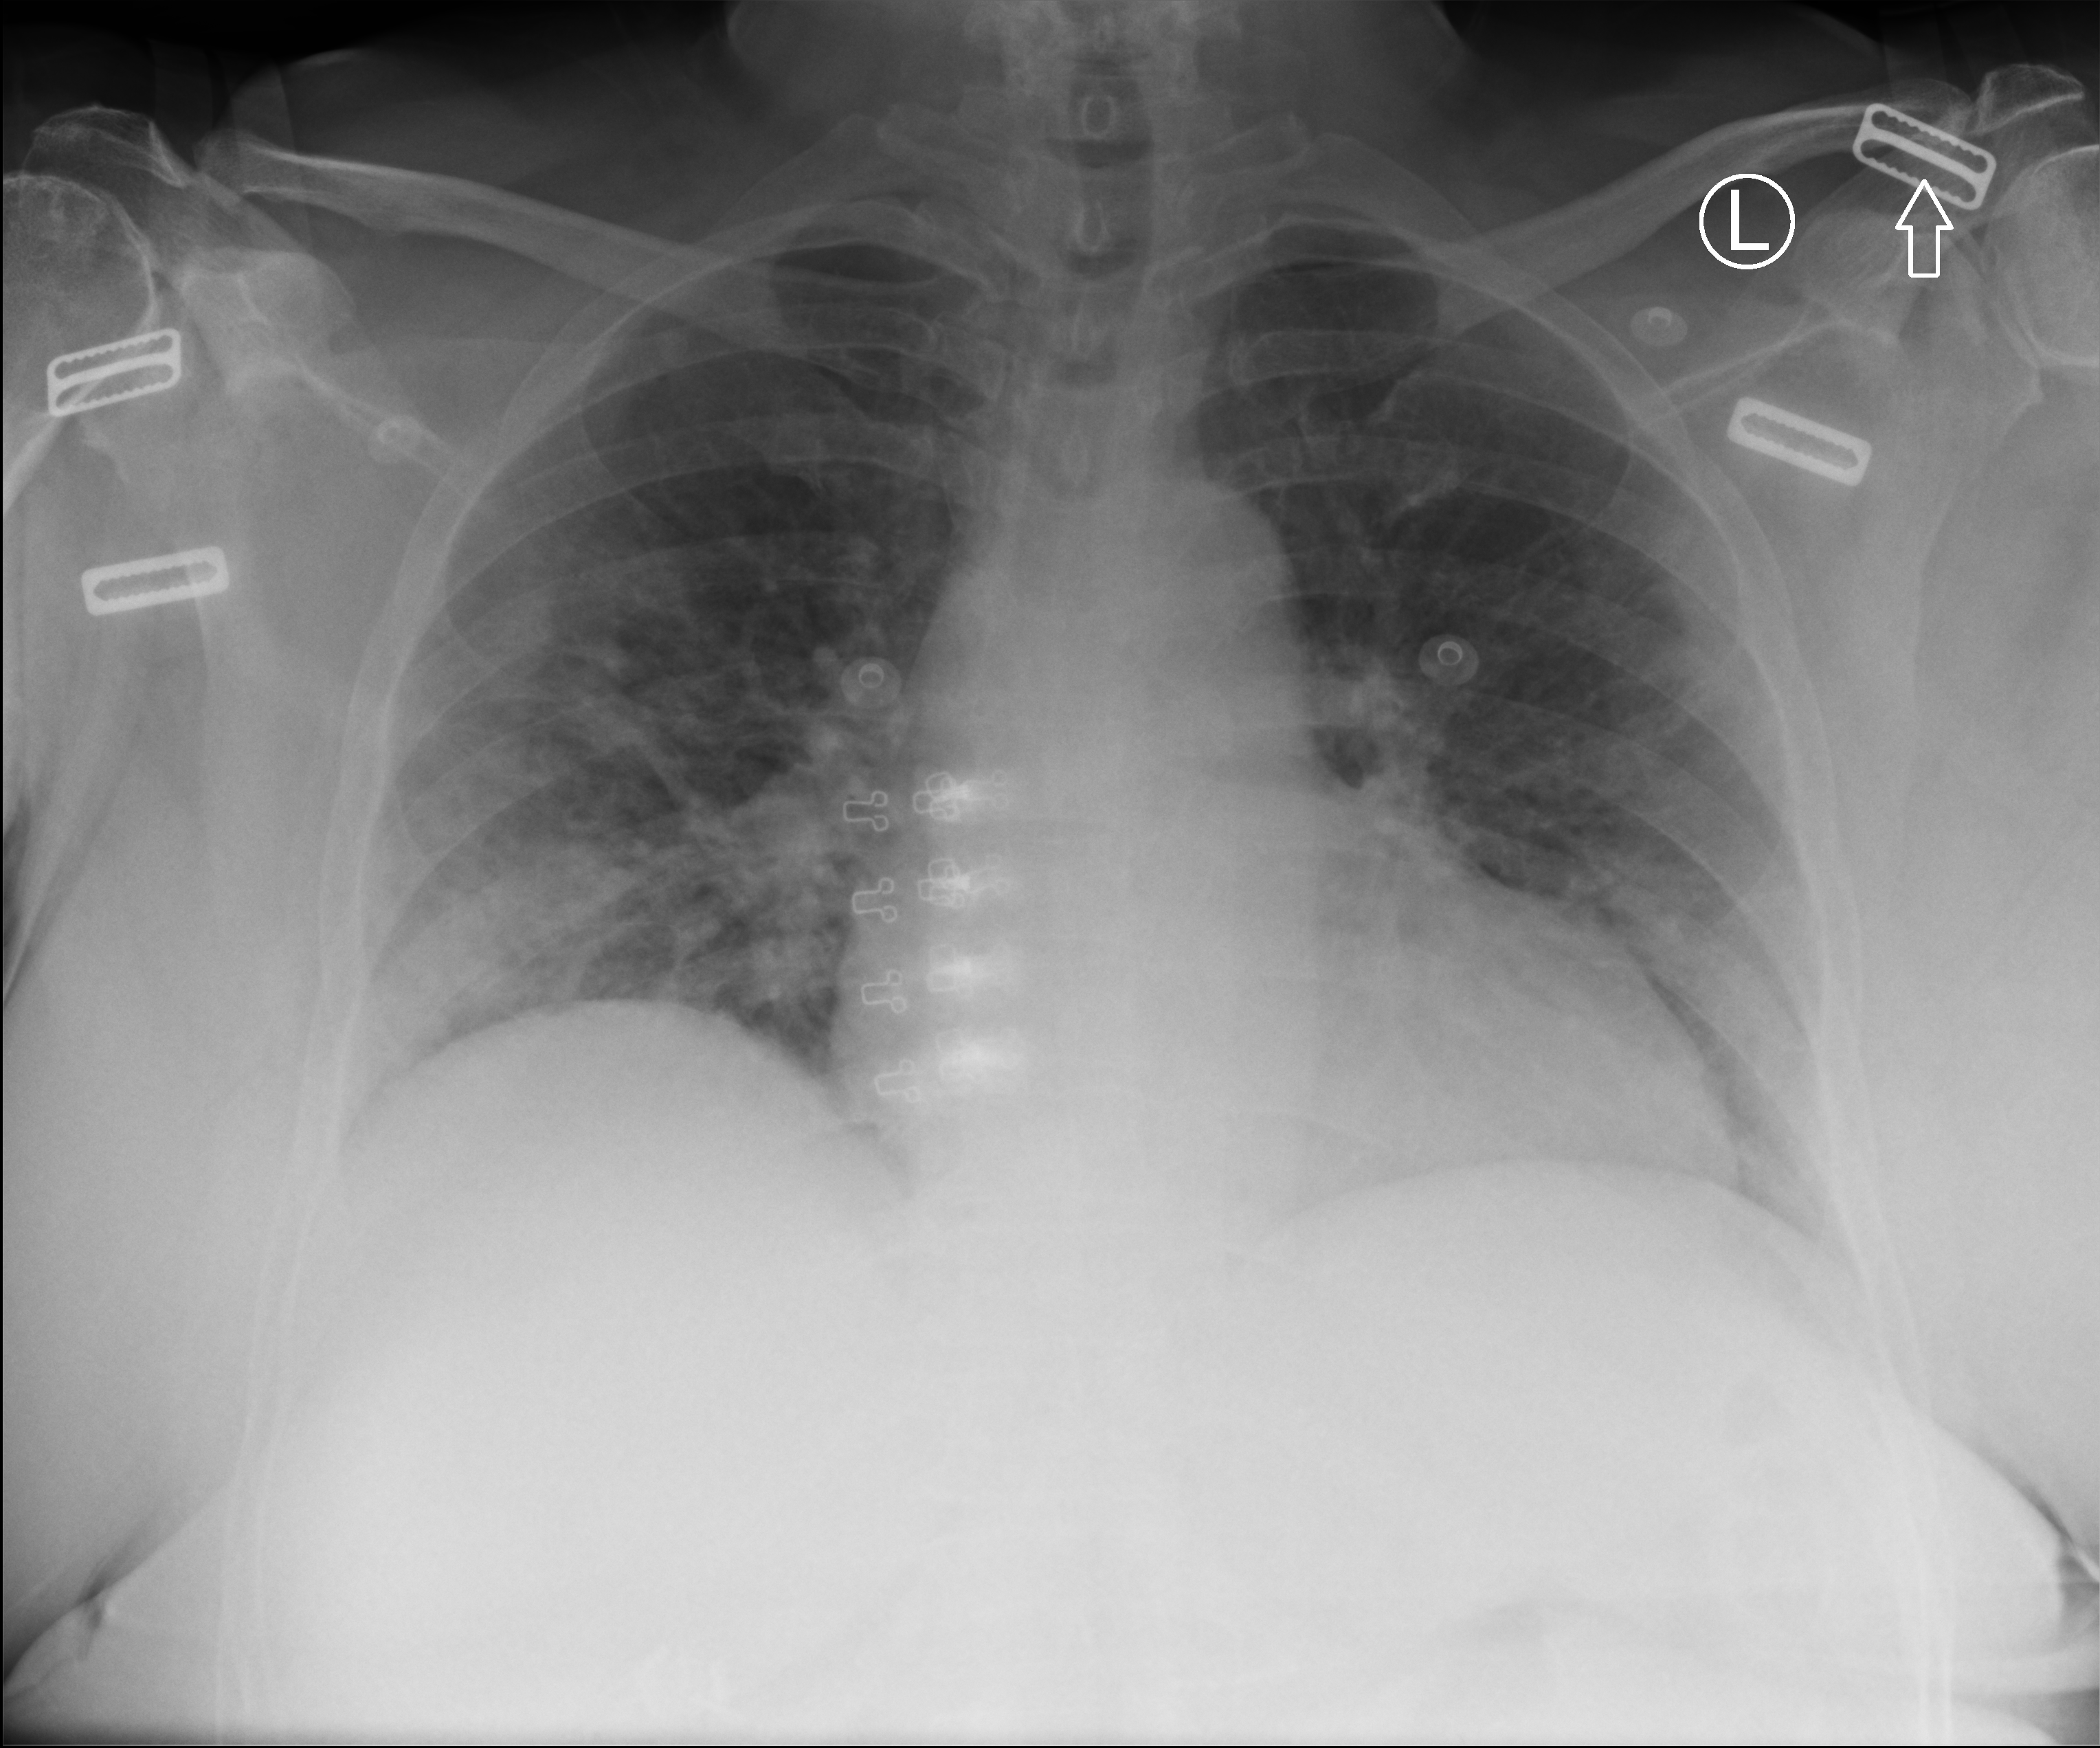
Chest X-ray (portable); anteroposterior (AP) projection. Patient hospitalised with COVID-19; female, aged 60–74 years.
From the hospital-stay record, not from the radiograph (when in the stay this image was taken is not recorded):
- admitted to intensive care during this hospital stay: no
- length of hospital stay: 7 days
- mechanically ventilated during this hospital stay: no